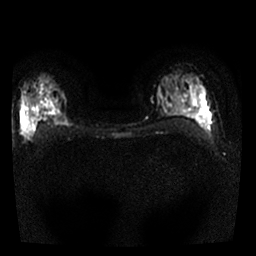
Breast MRI, one axial slice; slice 17 of 25 in the series (ordered by position); diffusion-weighted series; image 2 of 4 stored at this slice position (different b-values; order by instance number); 1.5 T; 4 mm slice thickness; 256 × 256 image matrix, field of view 300 × 300 mm. Female patient.
Structures marked on this image (expert manual segmentation):
- tumour on diffusion-weighted imaging: box from (x=21, y=84) to (x=65, y=137) px